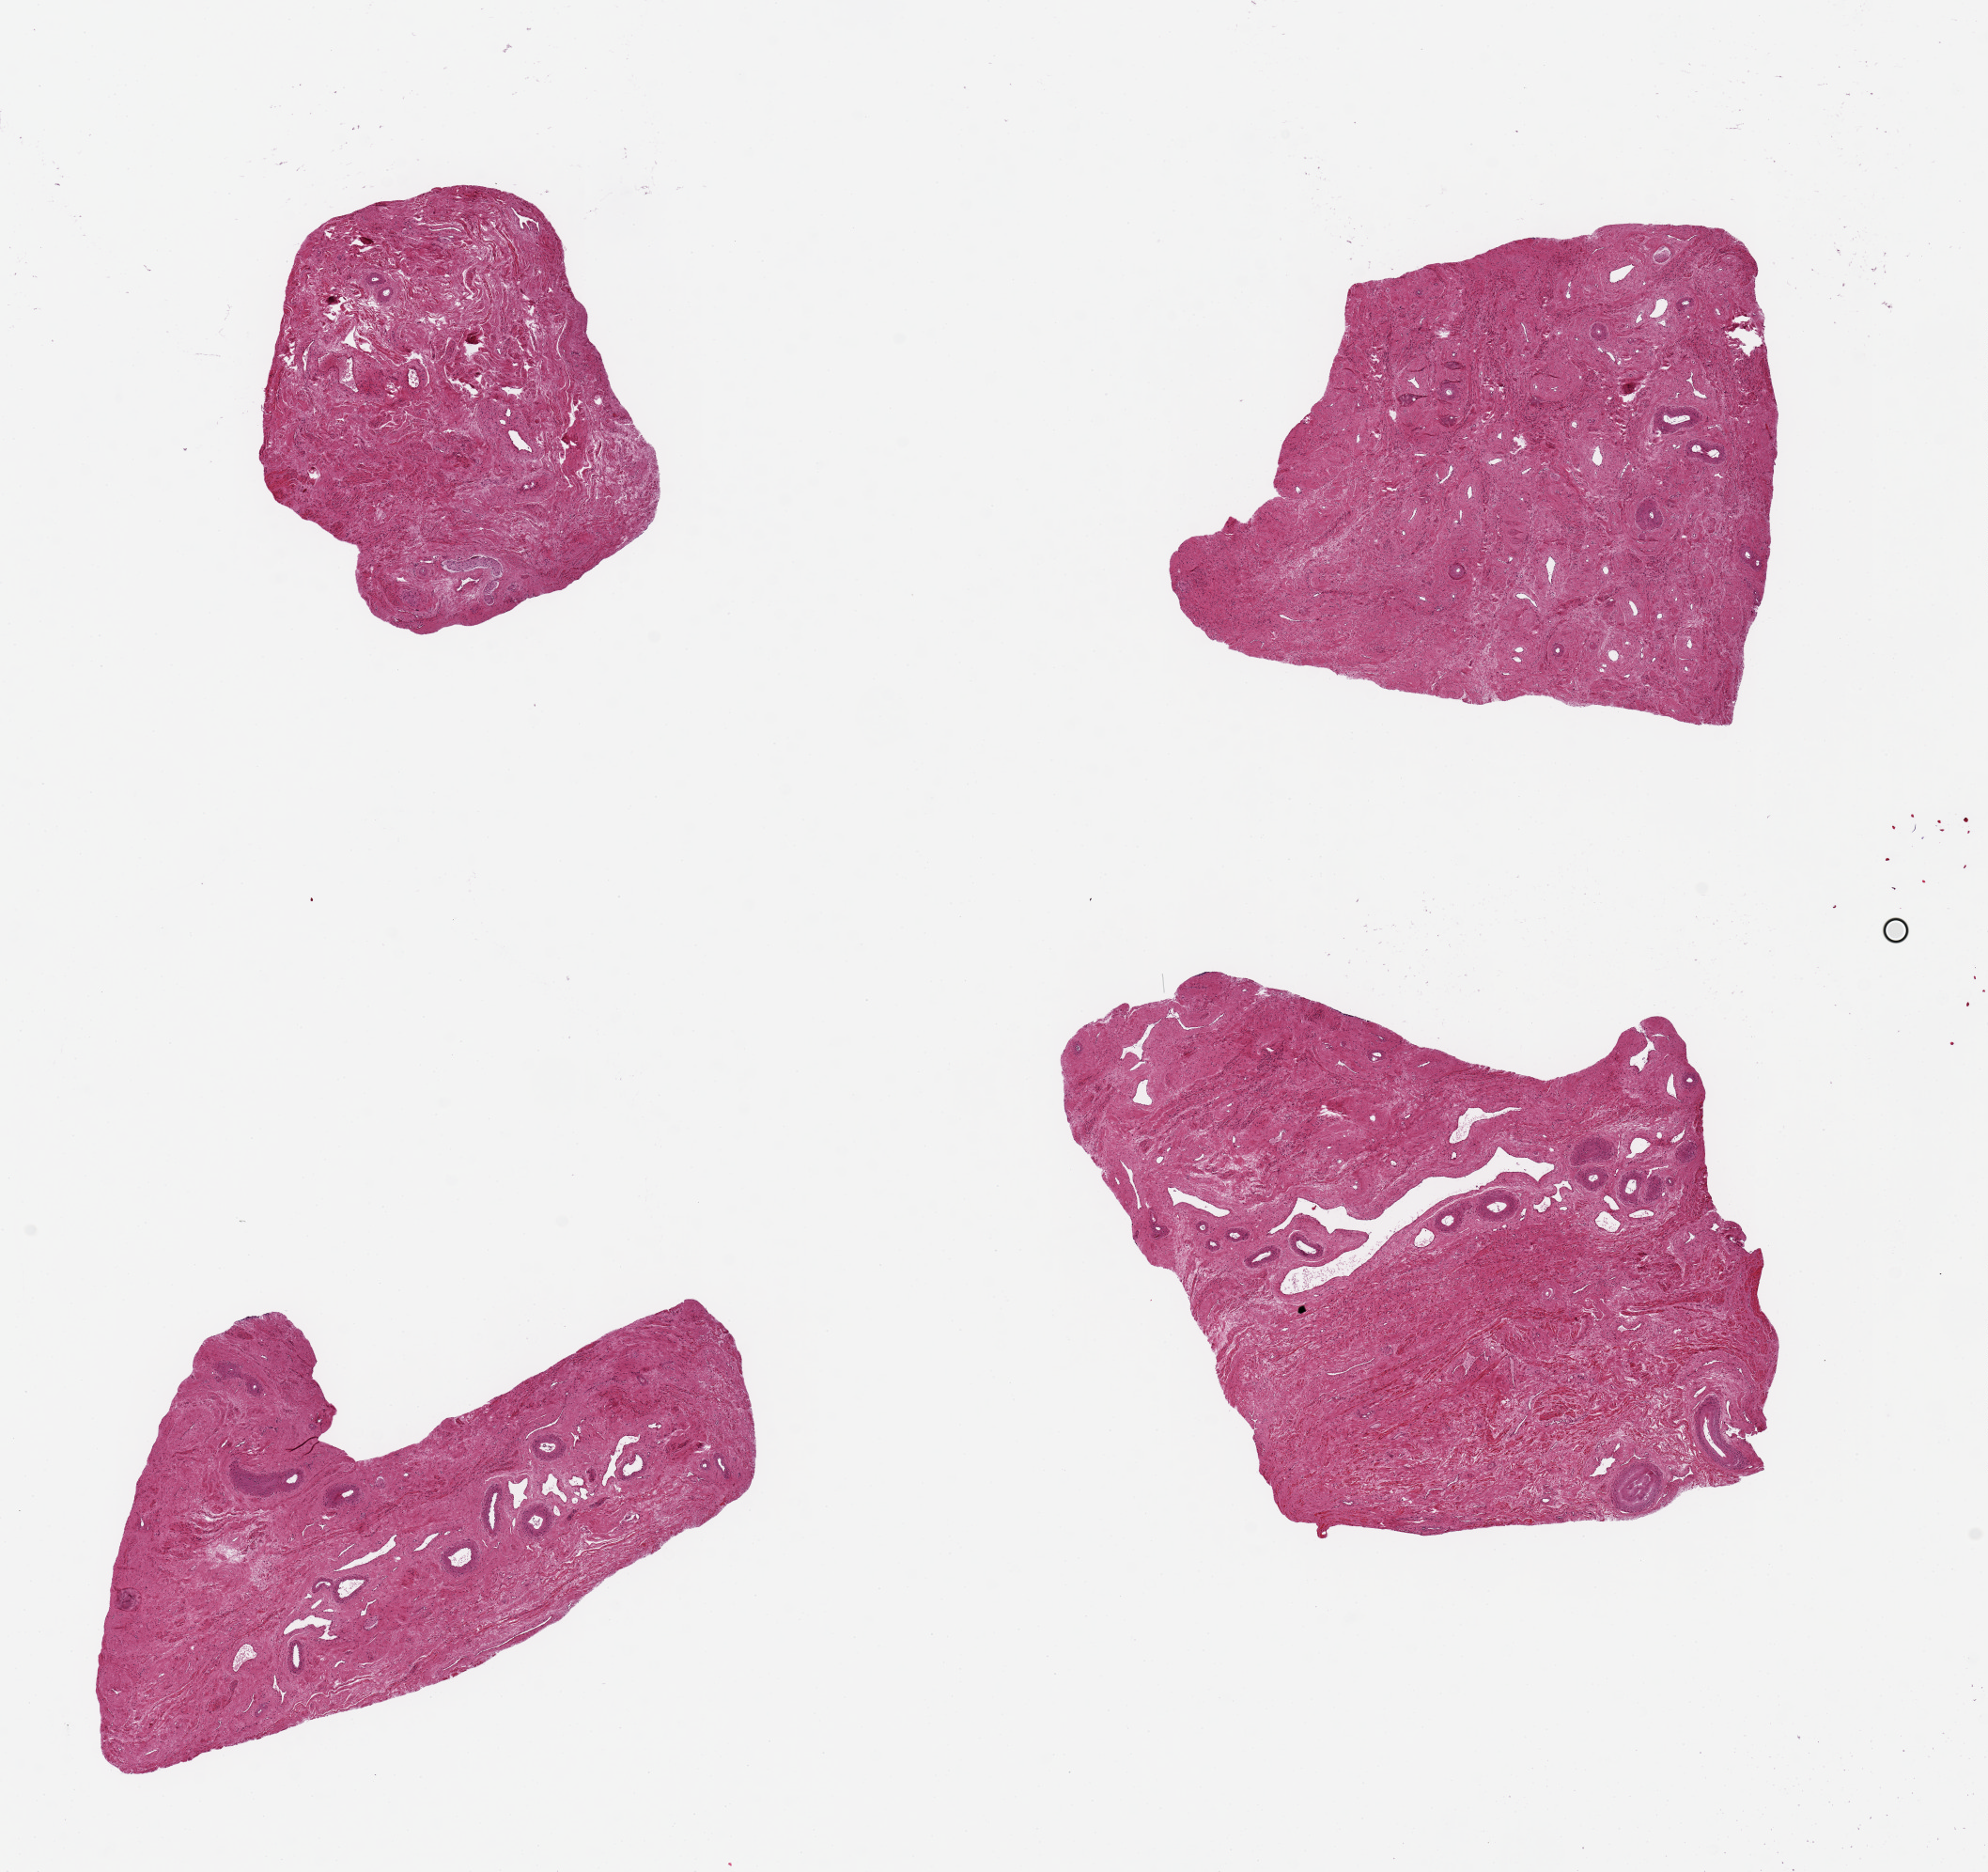
Whole-slide image, hematoxylin and eosin (H&E) stain — low-resolution overview of the scanned area, about 16.7 x 15.8 mm (from a 20x scan); PAXgene-fixed, paraffin-embedded tissue; sampled site (target tissue): exocervix; donor tissue sample. Female donor.
Review note (as recorded): 4 pieces up to 5x5 mm; none has squamous or glandular elements; consider it ectocervix.